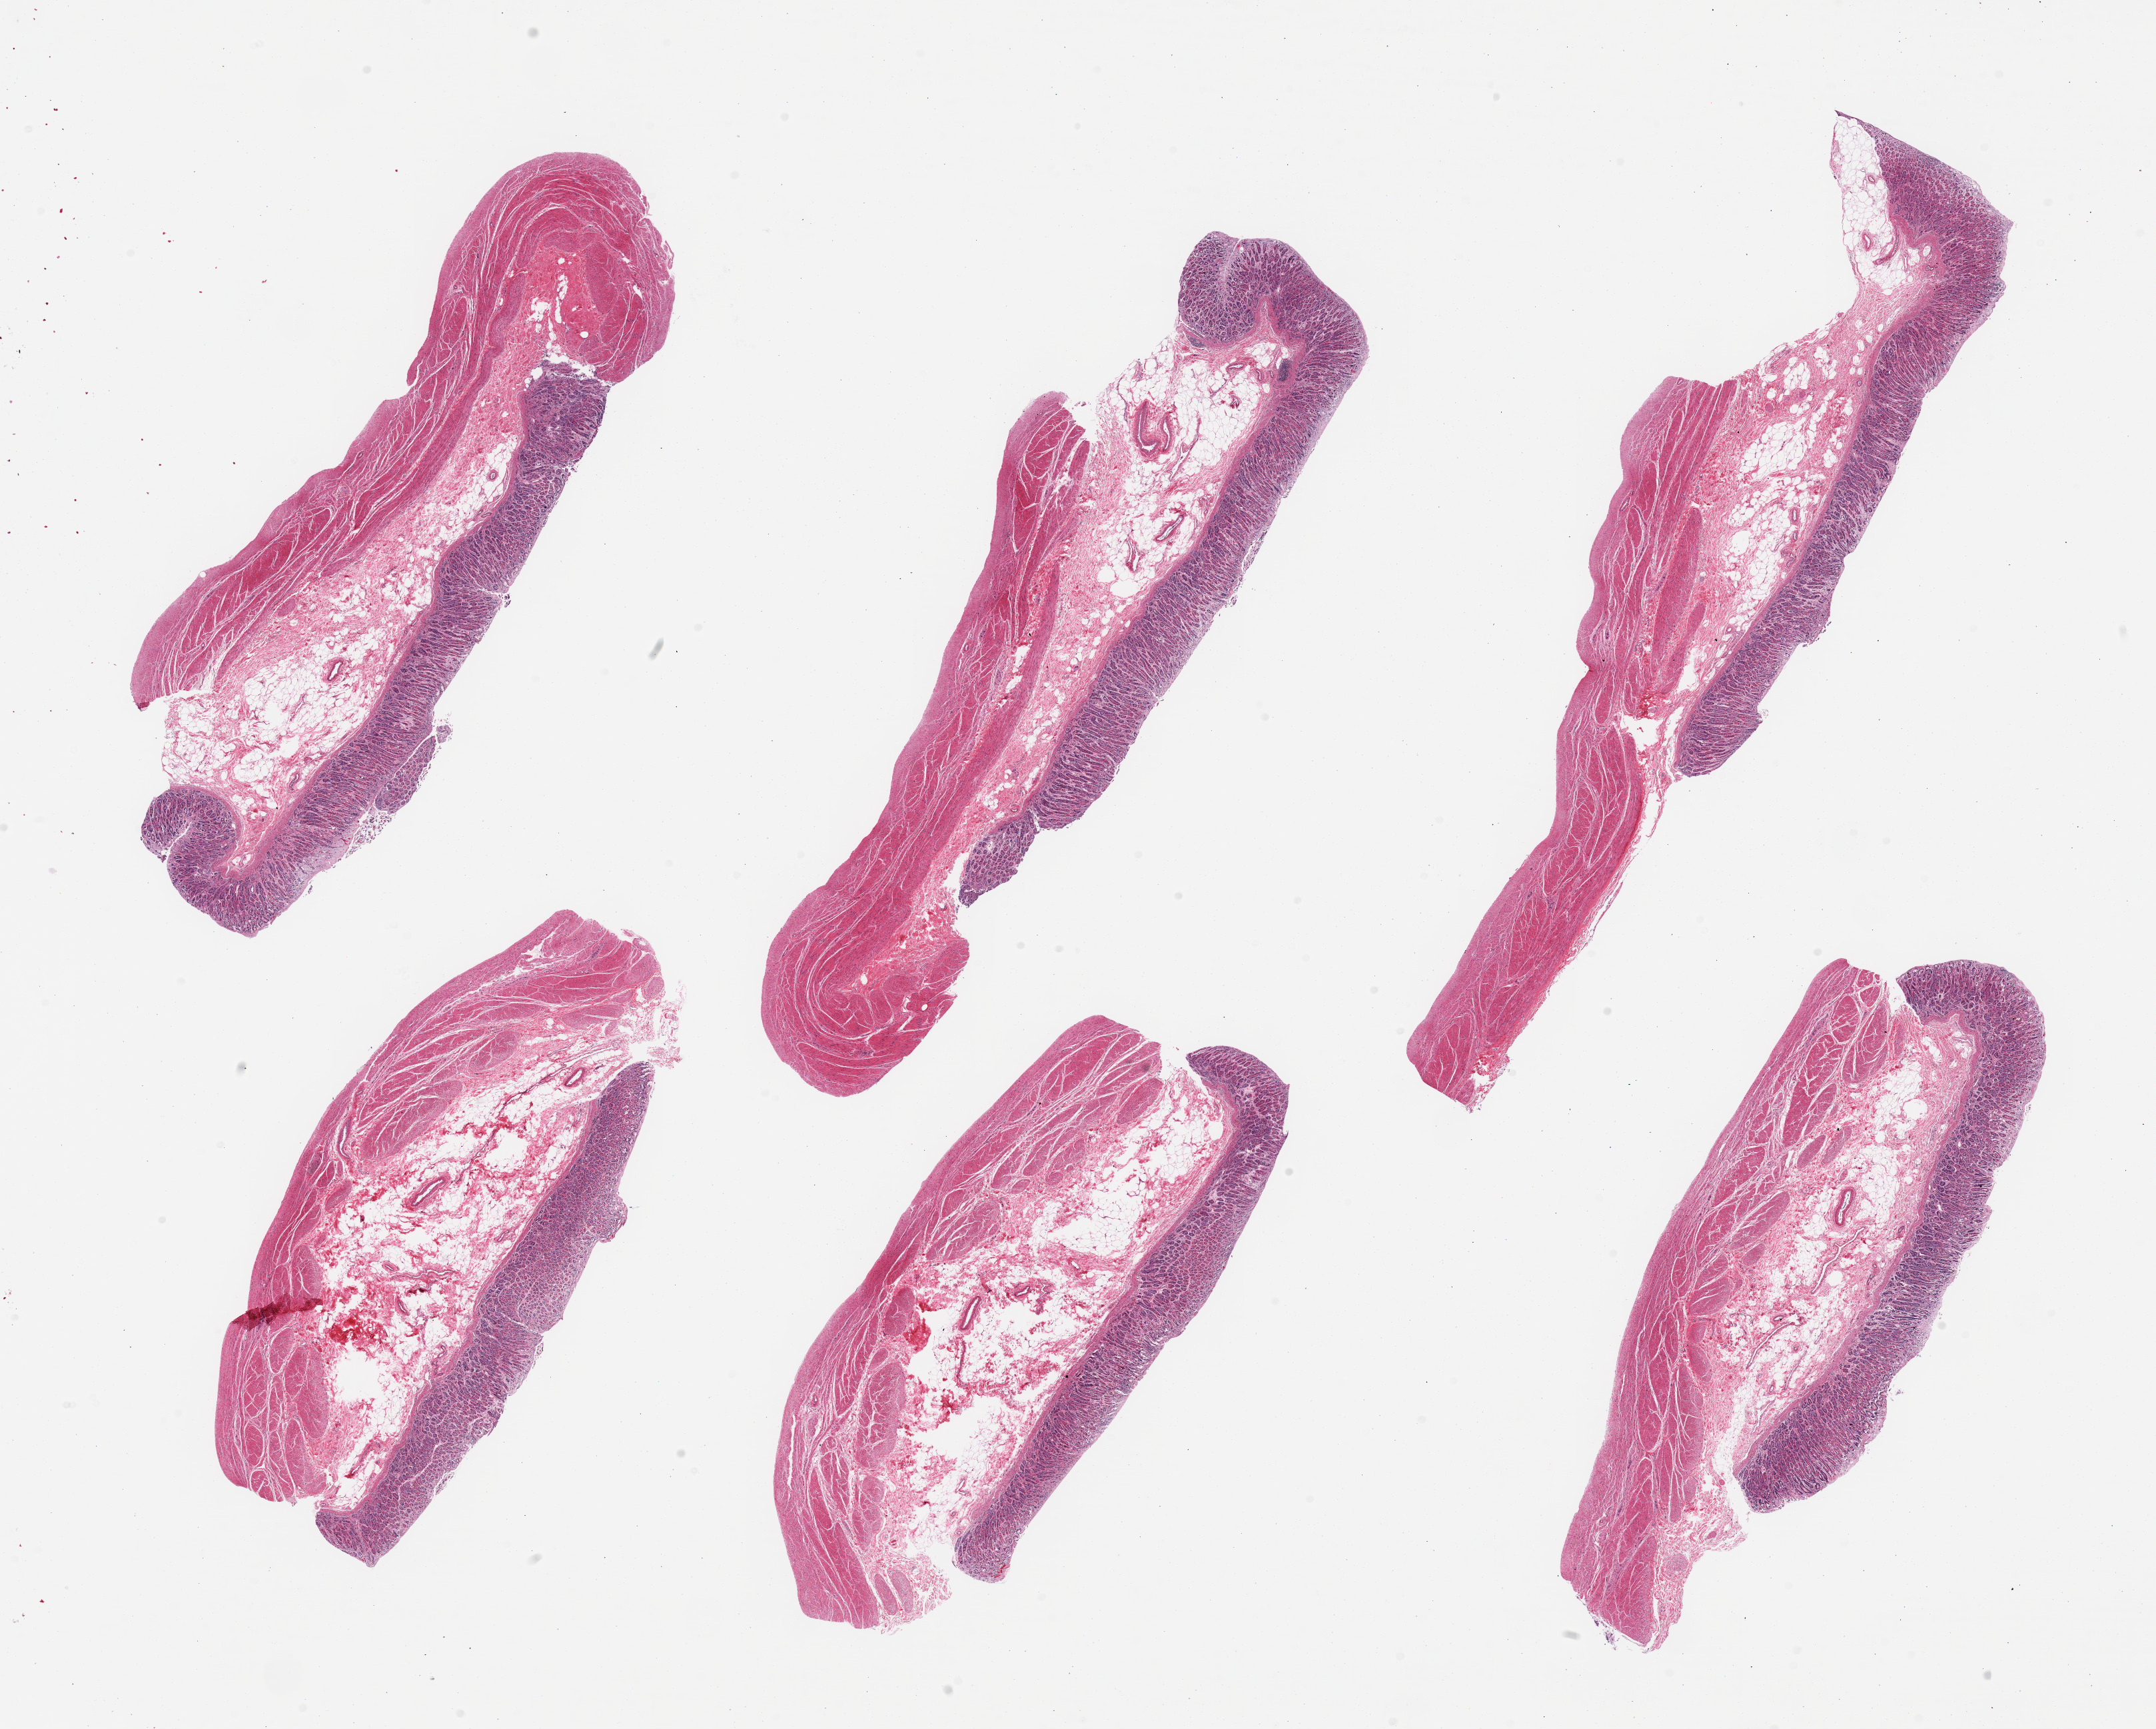
Digitized haematoxylin and eosin-stained section, brightfield, low-resolution overview of the scanned area, about 25.6 x 20.5 mm. PAXgene-fixed, paraffin-embedded tissue. Target tissue: stomach. Tissue donor sample.
• pathologist's review note for this sample: 6 pieces, target mucosa up to ~1mm, ~25-30% thickness. Luminal surface more autolyzed